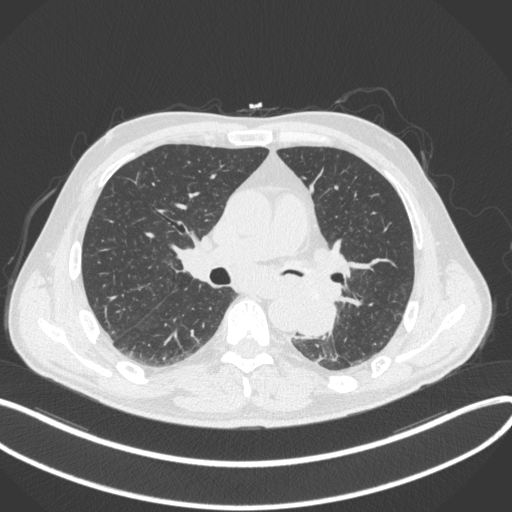
Chest CT, one axial slice; position 196 of 328 along the scan axis; reconstruction kernel B31f; 120 kVp; lung window (W 1500 / L -600 HU); 1 mm slice thickness; 512 × 512 image matrix, field of view 400 × 400 mm. Male patient, age 59 years. From the clinical record (not read from this slice): clinical TNM (as recorded): T2a N2 M0.
Structures marked on this image (rectangle marked by the reading radiologist):
- lung tumour (recorded histology: squamous cell carcinoma): bounding box [x1, y1, x2, y2] px = [295, 286, 339, 342]